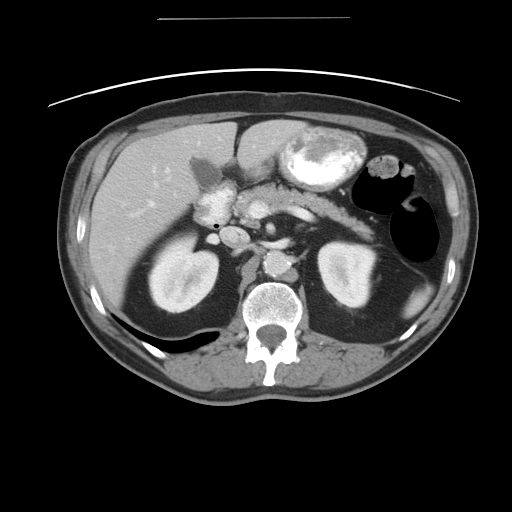
Contrast-enhanced abdominal CT, one axial slice. Position 24 of 49 along the scan axis. 120 kVp. Soft-tissue window (W 400 / L 40 HU). 512 × 512 image matrix. Male patient, age 57 years. Case-level facts recorded for this patient, not image findings: diagnosis: colorectal cancer liver metastases, imaged before liver resection; multiple liver metastases: yes; largest metastasis: 4 cm; disease in both lobes: no.
Structures marked on this image (outlined manually by an expert reader):
- hepatic veins: box from (x=109, y=141) to (x=199, y=247) px
- liver: (x=88, y=120)–(x=304, y=305)
- planned liver remnant (the part of the liver to remain after resection): (x=212, y=120)–(x=304, y=170)
- portal vein (with intrahepatic branches): (x=127, y=166)–(x=169, y=238)